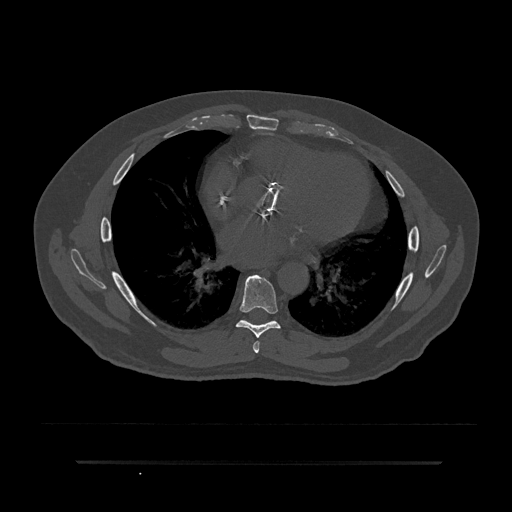
CT including the spine, one axial slice; slice 475 of 797 in the series (ordered by position); reconstruction kernel Br40s/3; bone window (W 1800 / L 400 HU); 0.5 mm slice thickness; 512 × 512 image matrix. Patient: male, 59 years. From the clinical record (not read from this slice): primary cancer: bile ducts; vertebrae with lytic lesions (as recorded): T10.
Outlined on this slice (semi-automatic segmentation, software-assisted and operator-edited):
- T6 vertebra: box from (x=253, y=341) to (x=260, y=353) px
- T7 vertebra: (x=236, y=274)–(x=281, y=338)
- T8 vertebra: (x=243, y=319)–(x=246, y=321)